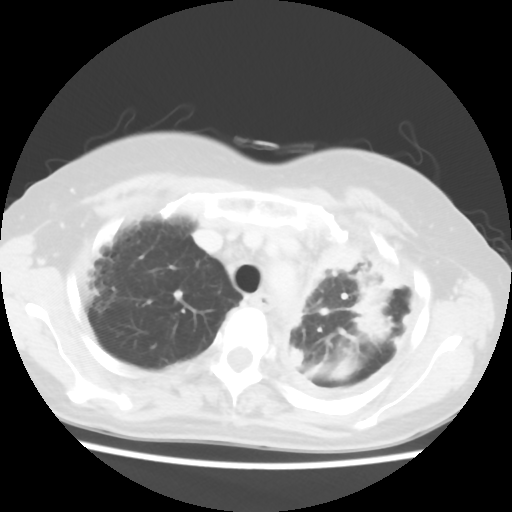
Chest CT, one axial slice; reconstruction kernel STANDARD; 120 kVp; lung window (W 1500 / L -600 HU); 512 × 512 image matrix, field of view 309 × 309 mm. Female patient, age 56 years. Case-level facts recorded for this patient, not image findings: clinical TNM (as recorded): T1c N0 M1.
Outlined on this slice (bounding box drawn by a radiologist):
- lung tumour (recorded histology: adenocarcinoma): bounding box <317,233,363,279> (left, top, right, bottom; pixels)